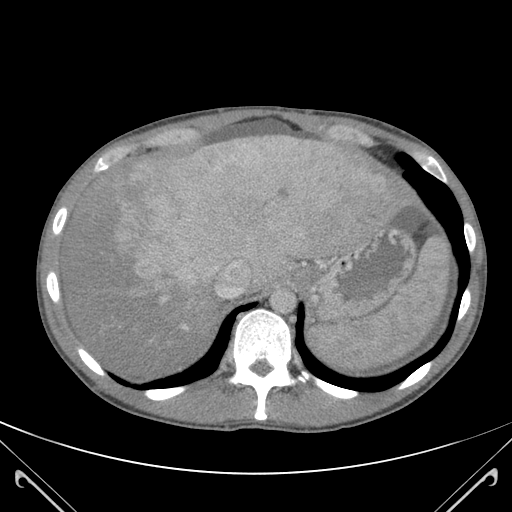
Contrast-enhanced abdominal CT (liver protocol), one axial slice; slice 95 of 118 in the series (ordered by position); 120 kVp; soft-tissue window (W 400 / L 40 HU); 3 mm slice thickness; 512 × 512 image matrix, field of view 380 × 380 mm. From the clinical record (not read from this slice): diagnosis: hepatocellular carcinoma (patient treated with transarterial chemoembolisation; whether this scan precedes or follows treatment is not stated here); TNM stage (as recorded): Stage-IIIB; Child-Pugh class: A; tumour nodularity: uninodular.
Annotated regions visible in this slice (semi-automatically segmented with operator editing):
- abdominal aorta: bounding box <273,289,295,312> (left, top, right, bottom; pixels)
- liver parenchyma outside the tumour (the mass and vessels are separate outlines, so this box may not span the whole liver): <64,136,408,374>
- mass: <99,136,367,298>
- liver vessels: <162,142,365,329>